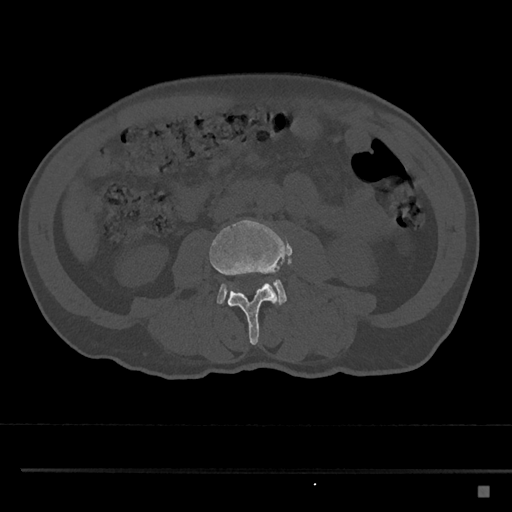
CT including the spine, one axial slice; slice 679 of 797 in the series (ordered by position); reconstruction kernel Br40s/3; bone window (W 1800 / L 400 HU); 0.5 mm slice thickness; 512 × 512 image matrix, field of view 391 × 391 mm. Patient: male, 59 years. From the clinical record (not read from this slice): primary cancer: prostate.
Structures marked on this image (semi-automatic segmentation, software-assisted and operator-edited):
- L3 vertebra: bounding box <209,219,286,345> (left, top, right, bottom; pixels)
- L4 vertebra: <216,279,287,305>